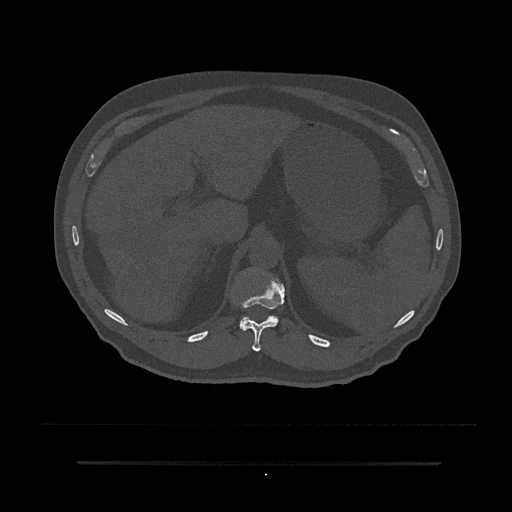
CT including the spine, one axial slice; position 249 of 797 along the scan axis; reconstruction kernel Br40s/3; 120 kVp; bone window (W 1800 / L 400 HU); 512 × 512 image matrix. Male patient, age 59 years. From the clinical record (not read from this slice): primary cancer: bile ducts.
Outlined on this slice (semi-automatic segmentation, software-assisted and operator-edited):
- T11 vertebra: box from (x=241, y=279) to (x=284, y=352) px
- T12 vertebra: (x=240, y=316)–(x=279, y=328)